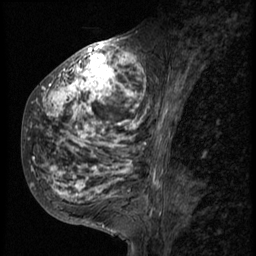
Breast MRI (dynamic contrast-enhanced), one sagittal slice; slice 26 of 58 in the series (ordered by position); 3 images stored at this slice position (order not interpretable as contrast timing); 1.5 T; TE 4.2 ms, TR 9 ms; 2.5 mm slice thickness; 256 × 256 image matrix, field of view 180 × 180 mm. Patient: female, 50 years. From the clinical record (not read from this slice): setting: breast cancer imaged before/during neoadjuvant chemotherapy; receptor status: triple-negative.
Annotated regions visible in this slice (semi-automatic segmentation, software-assisted and operator-edited):
- analysis volume of interest (the breast-tissue region the enhancement analysis was run in; not a lesion): box from (x=23, y=48) to (x=162, y=214) px
- tumour enhancement mask (voxels above the 140 % enhancement threshold inside the analysis volume of interest): (x=31, y=48)–(x=162, y=213)